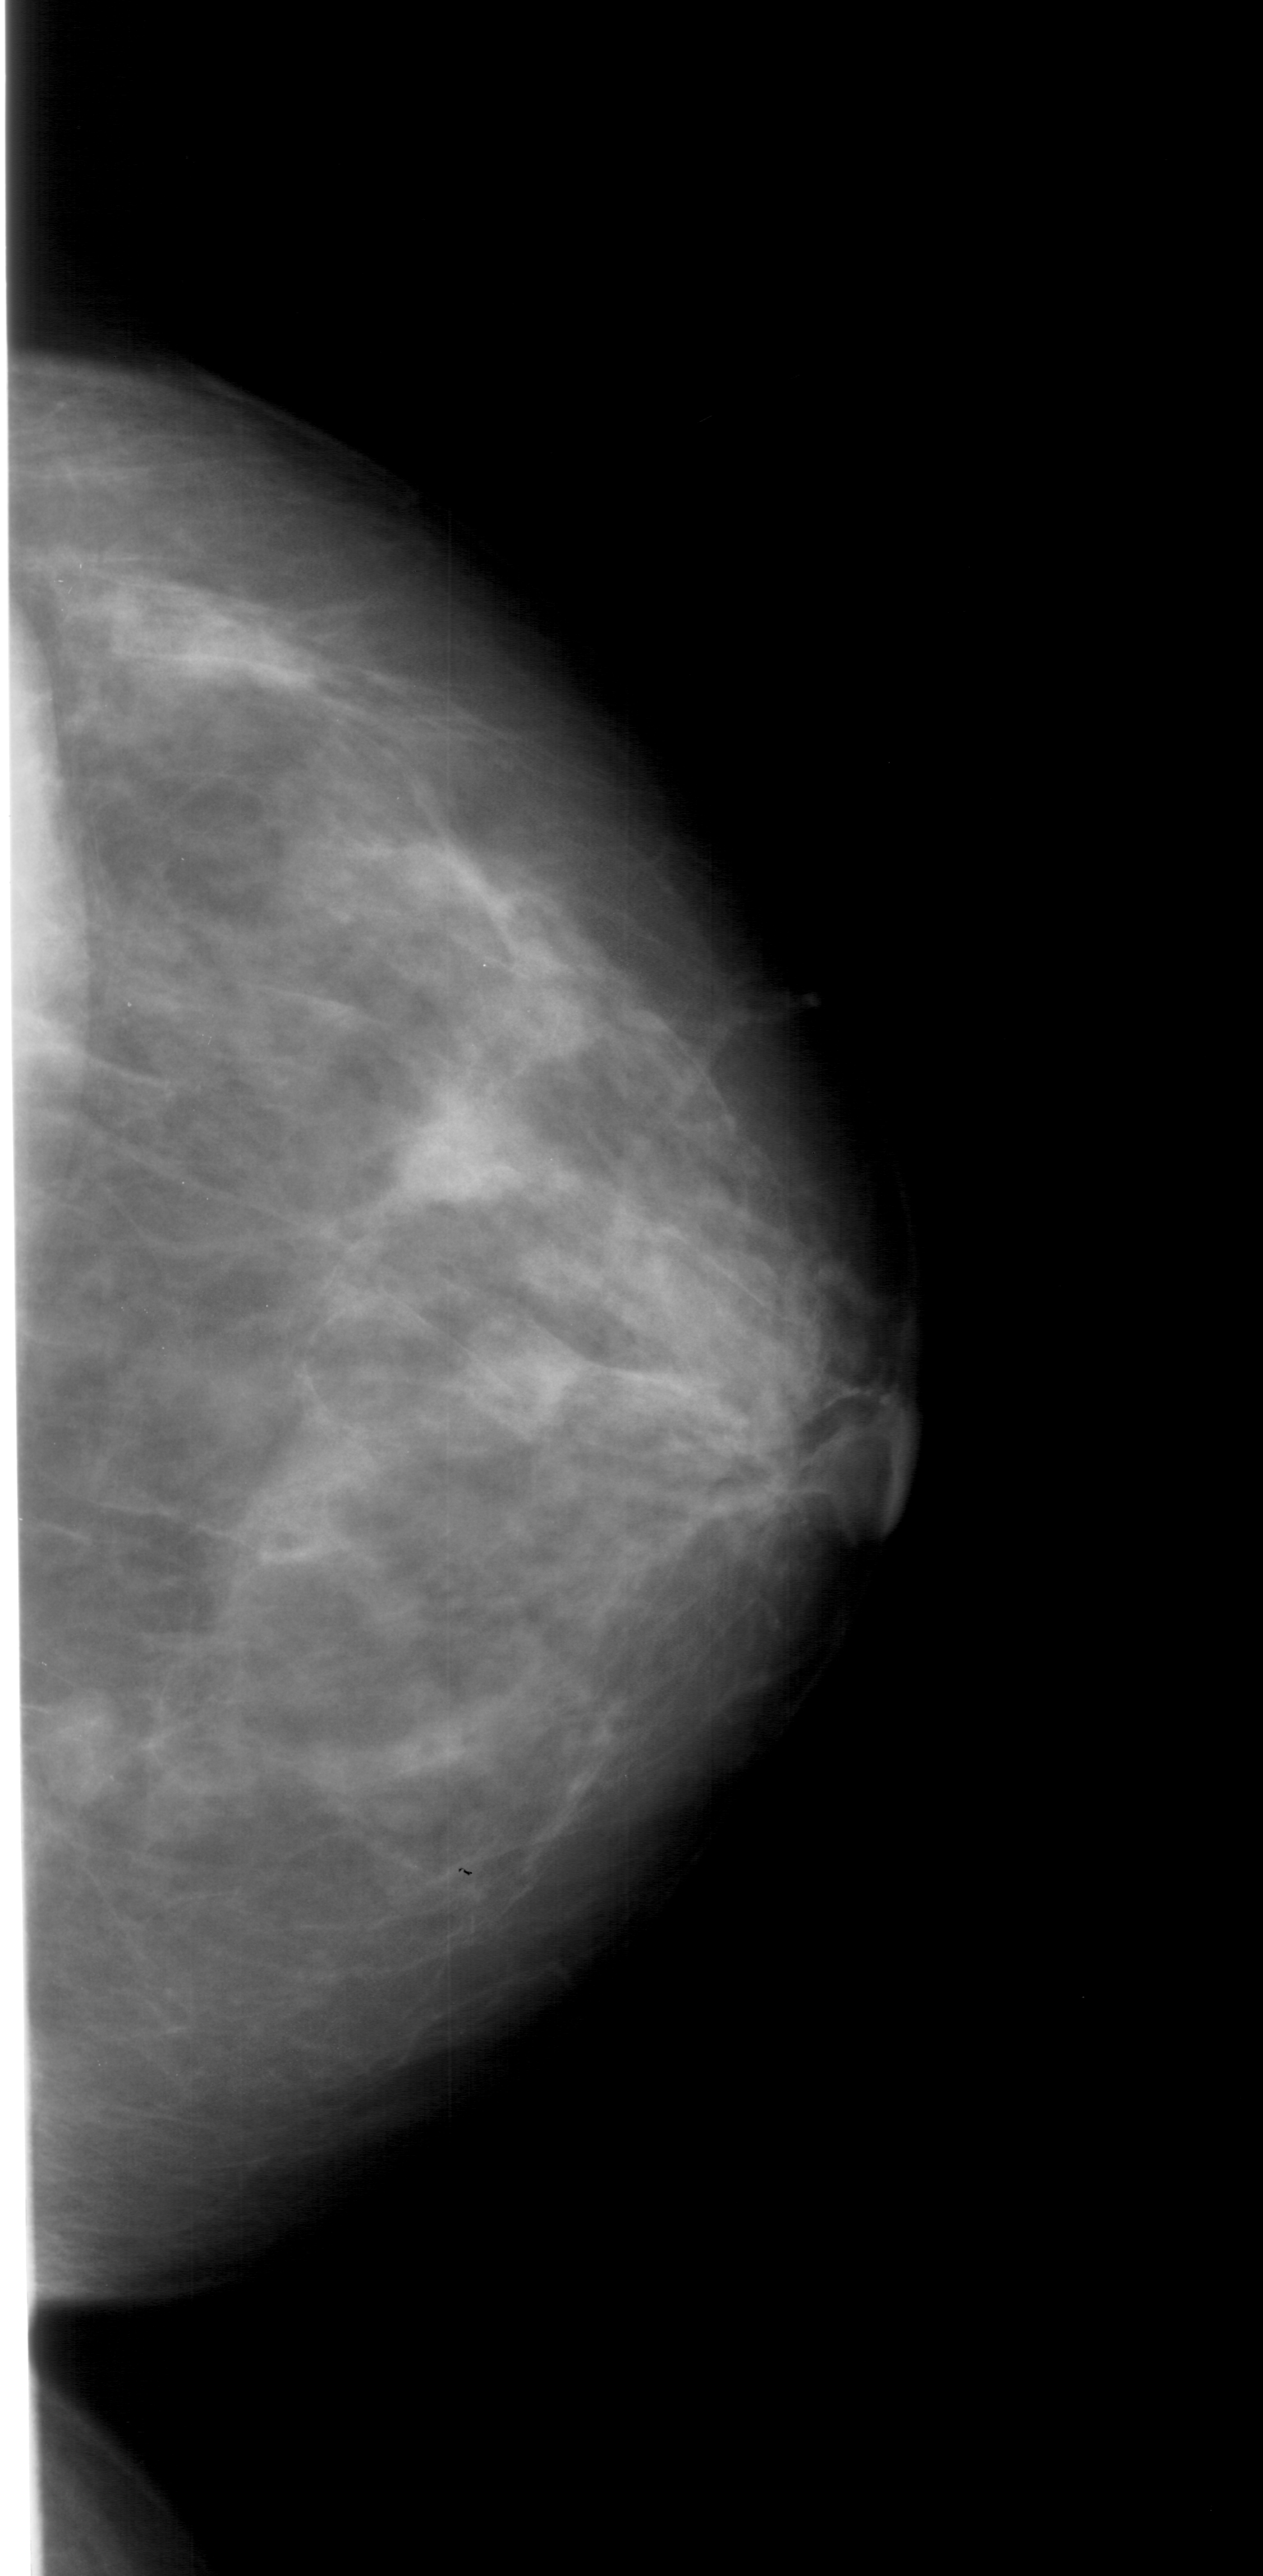
Scanned film-screen mammogram; right breast; craniocaudal (CC) view; breast composition: heterogeneously dense (BI-RADS density category 3 of 4); 1263 × 2576 image matrix.
Expert-marked regions of interest on this film, with their recorded descriptors:
- mass, shape lobulated, margins obscured; BI-RADS assessment category 3; subtlety rating 3 on a 1 (subtle) to 5 (obvious) scale; pathology result (as recorded, not read from the image): benign: box from (x=28, y=1680) to (x=132, y=1811) px